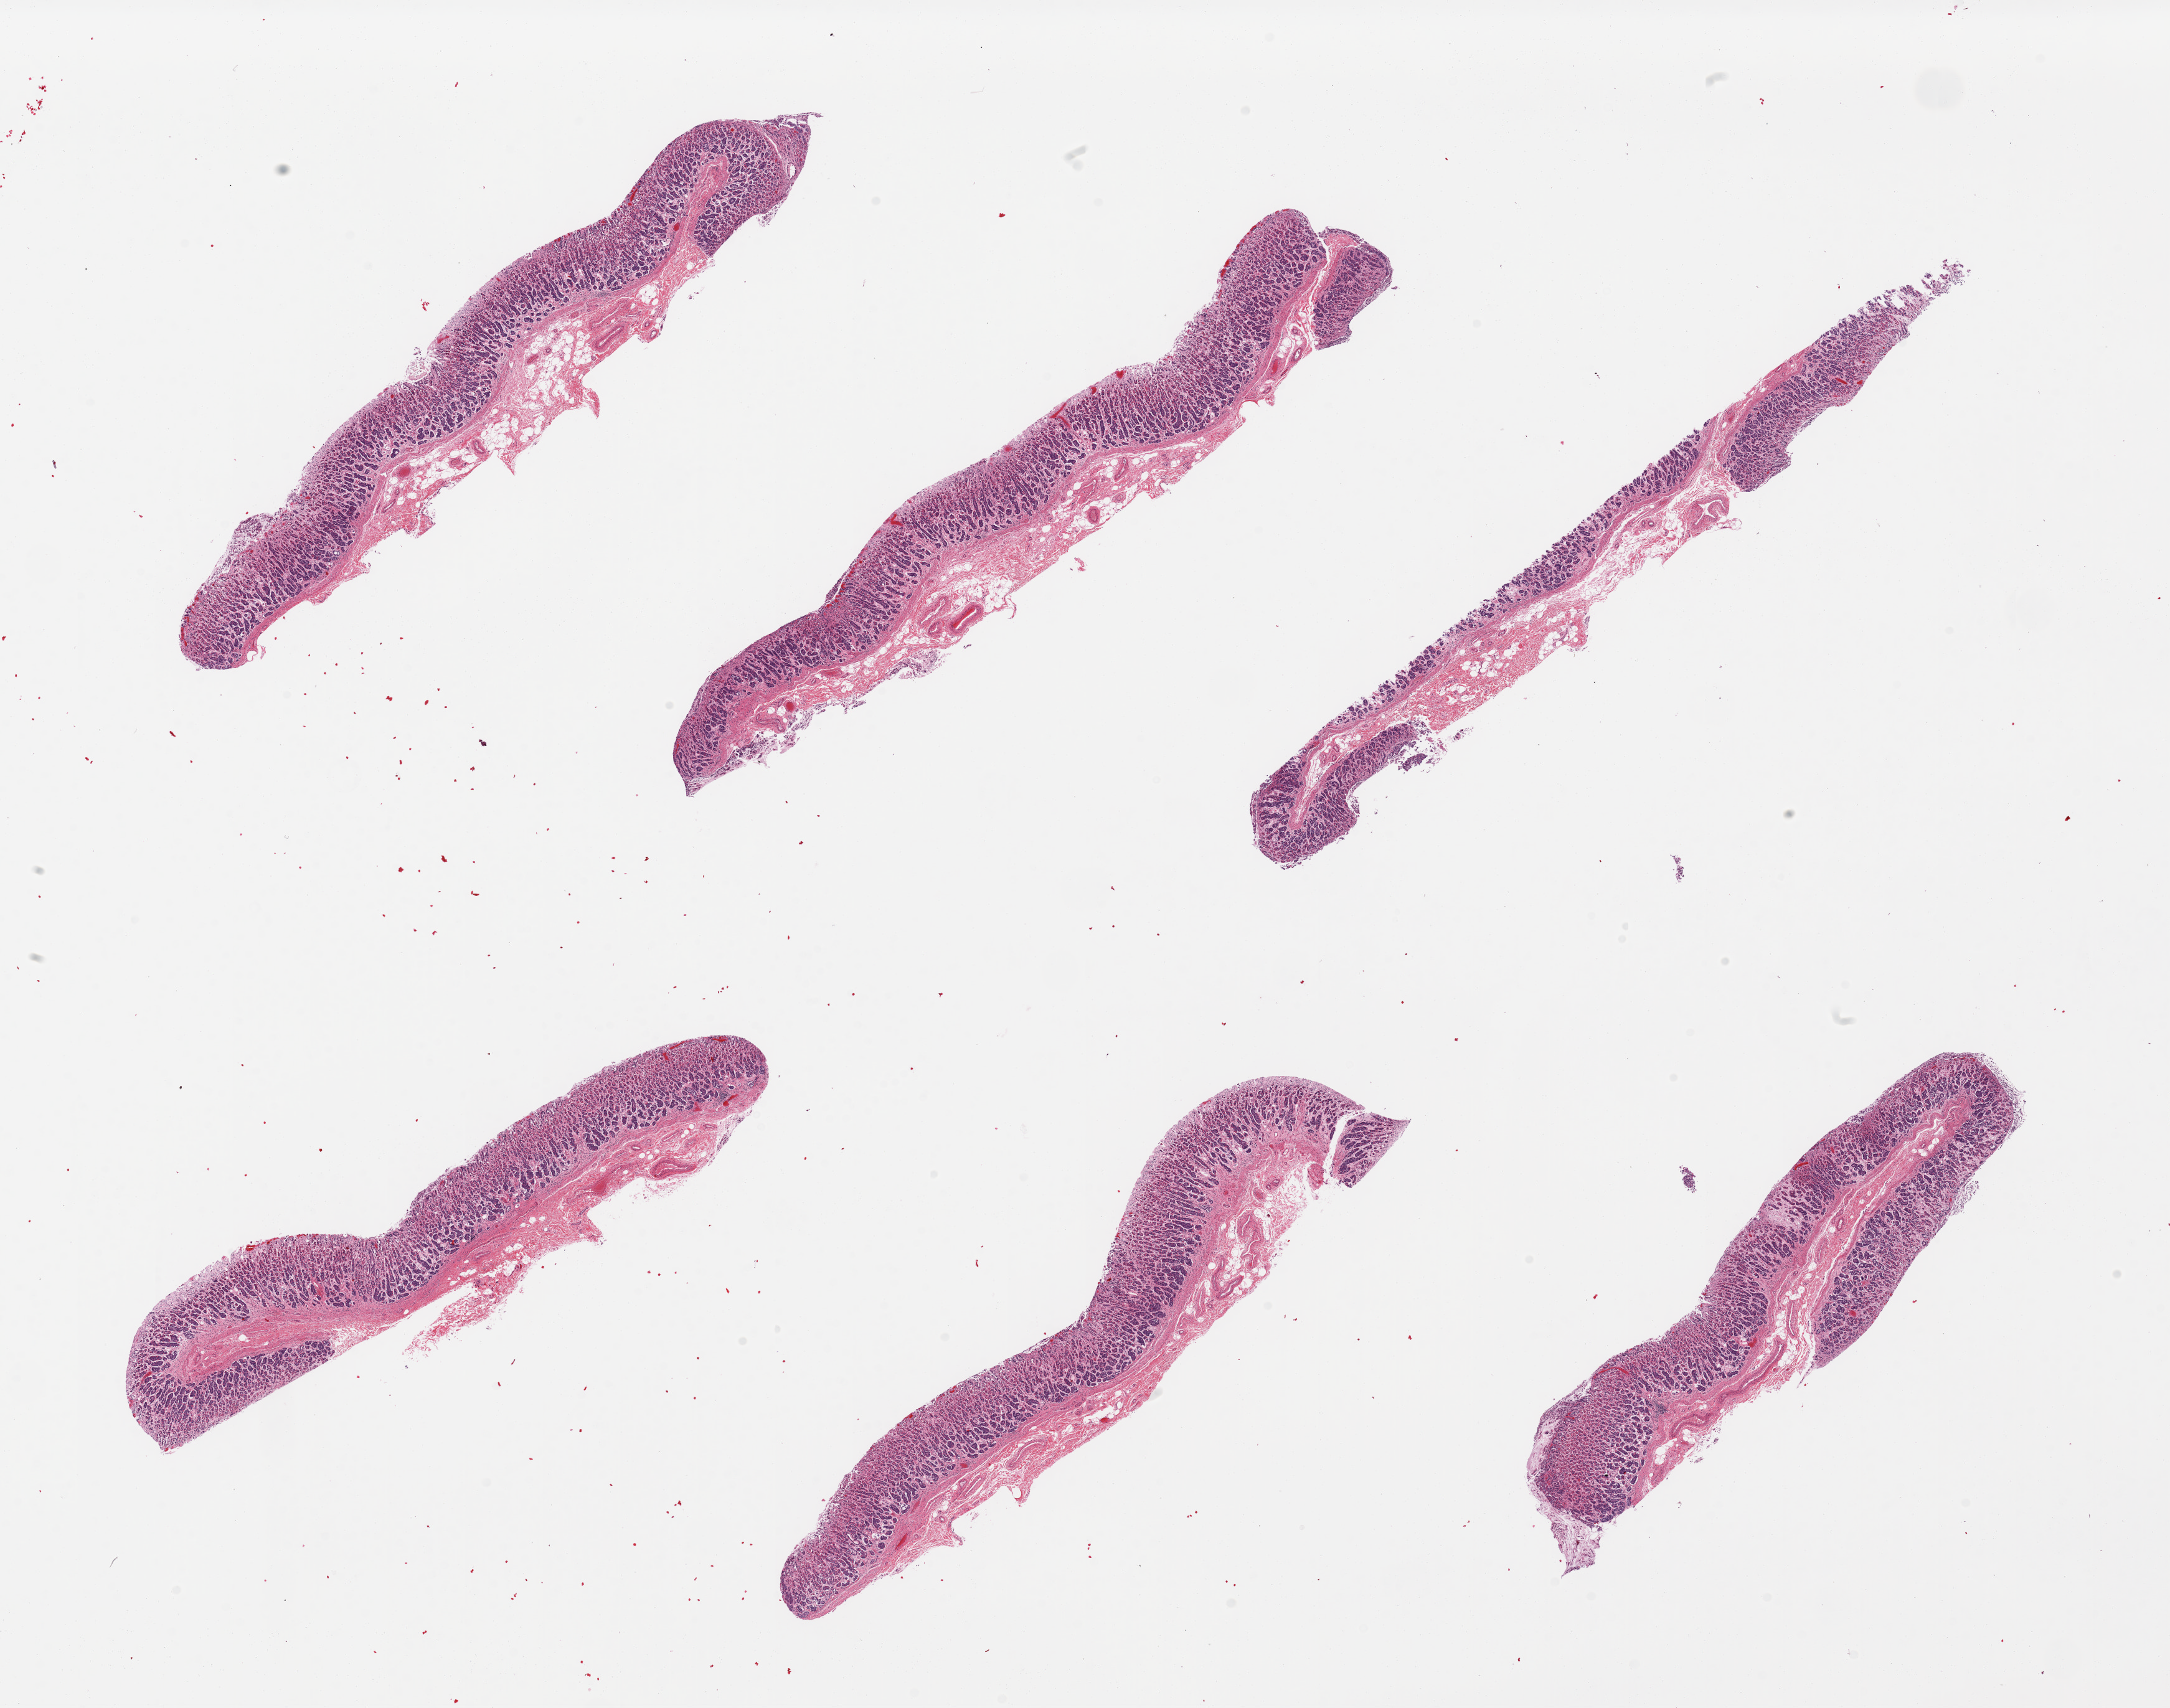
H&E whole-slide image — whole scanned area (about 27.6 x 21.7 mm) shown as a low-resolution overview, PAXgene-fixed, paraffin-embedded tissue, section of stomach (target tissue), donor tissue sample. Donor: female.
Reviewer comment on this tissue sample: 6 pieces, moderately autolyzed mucosa.